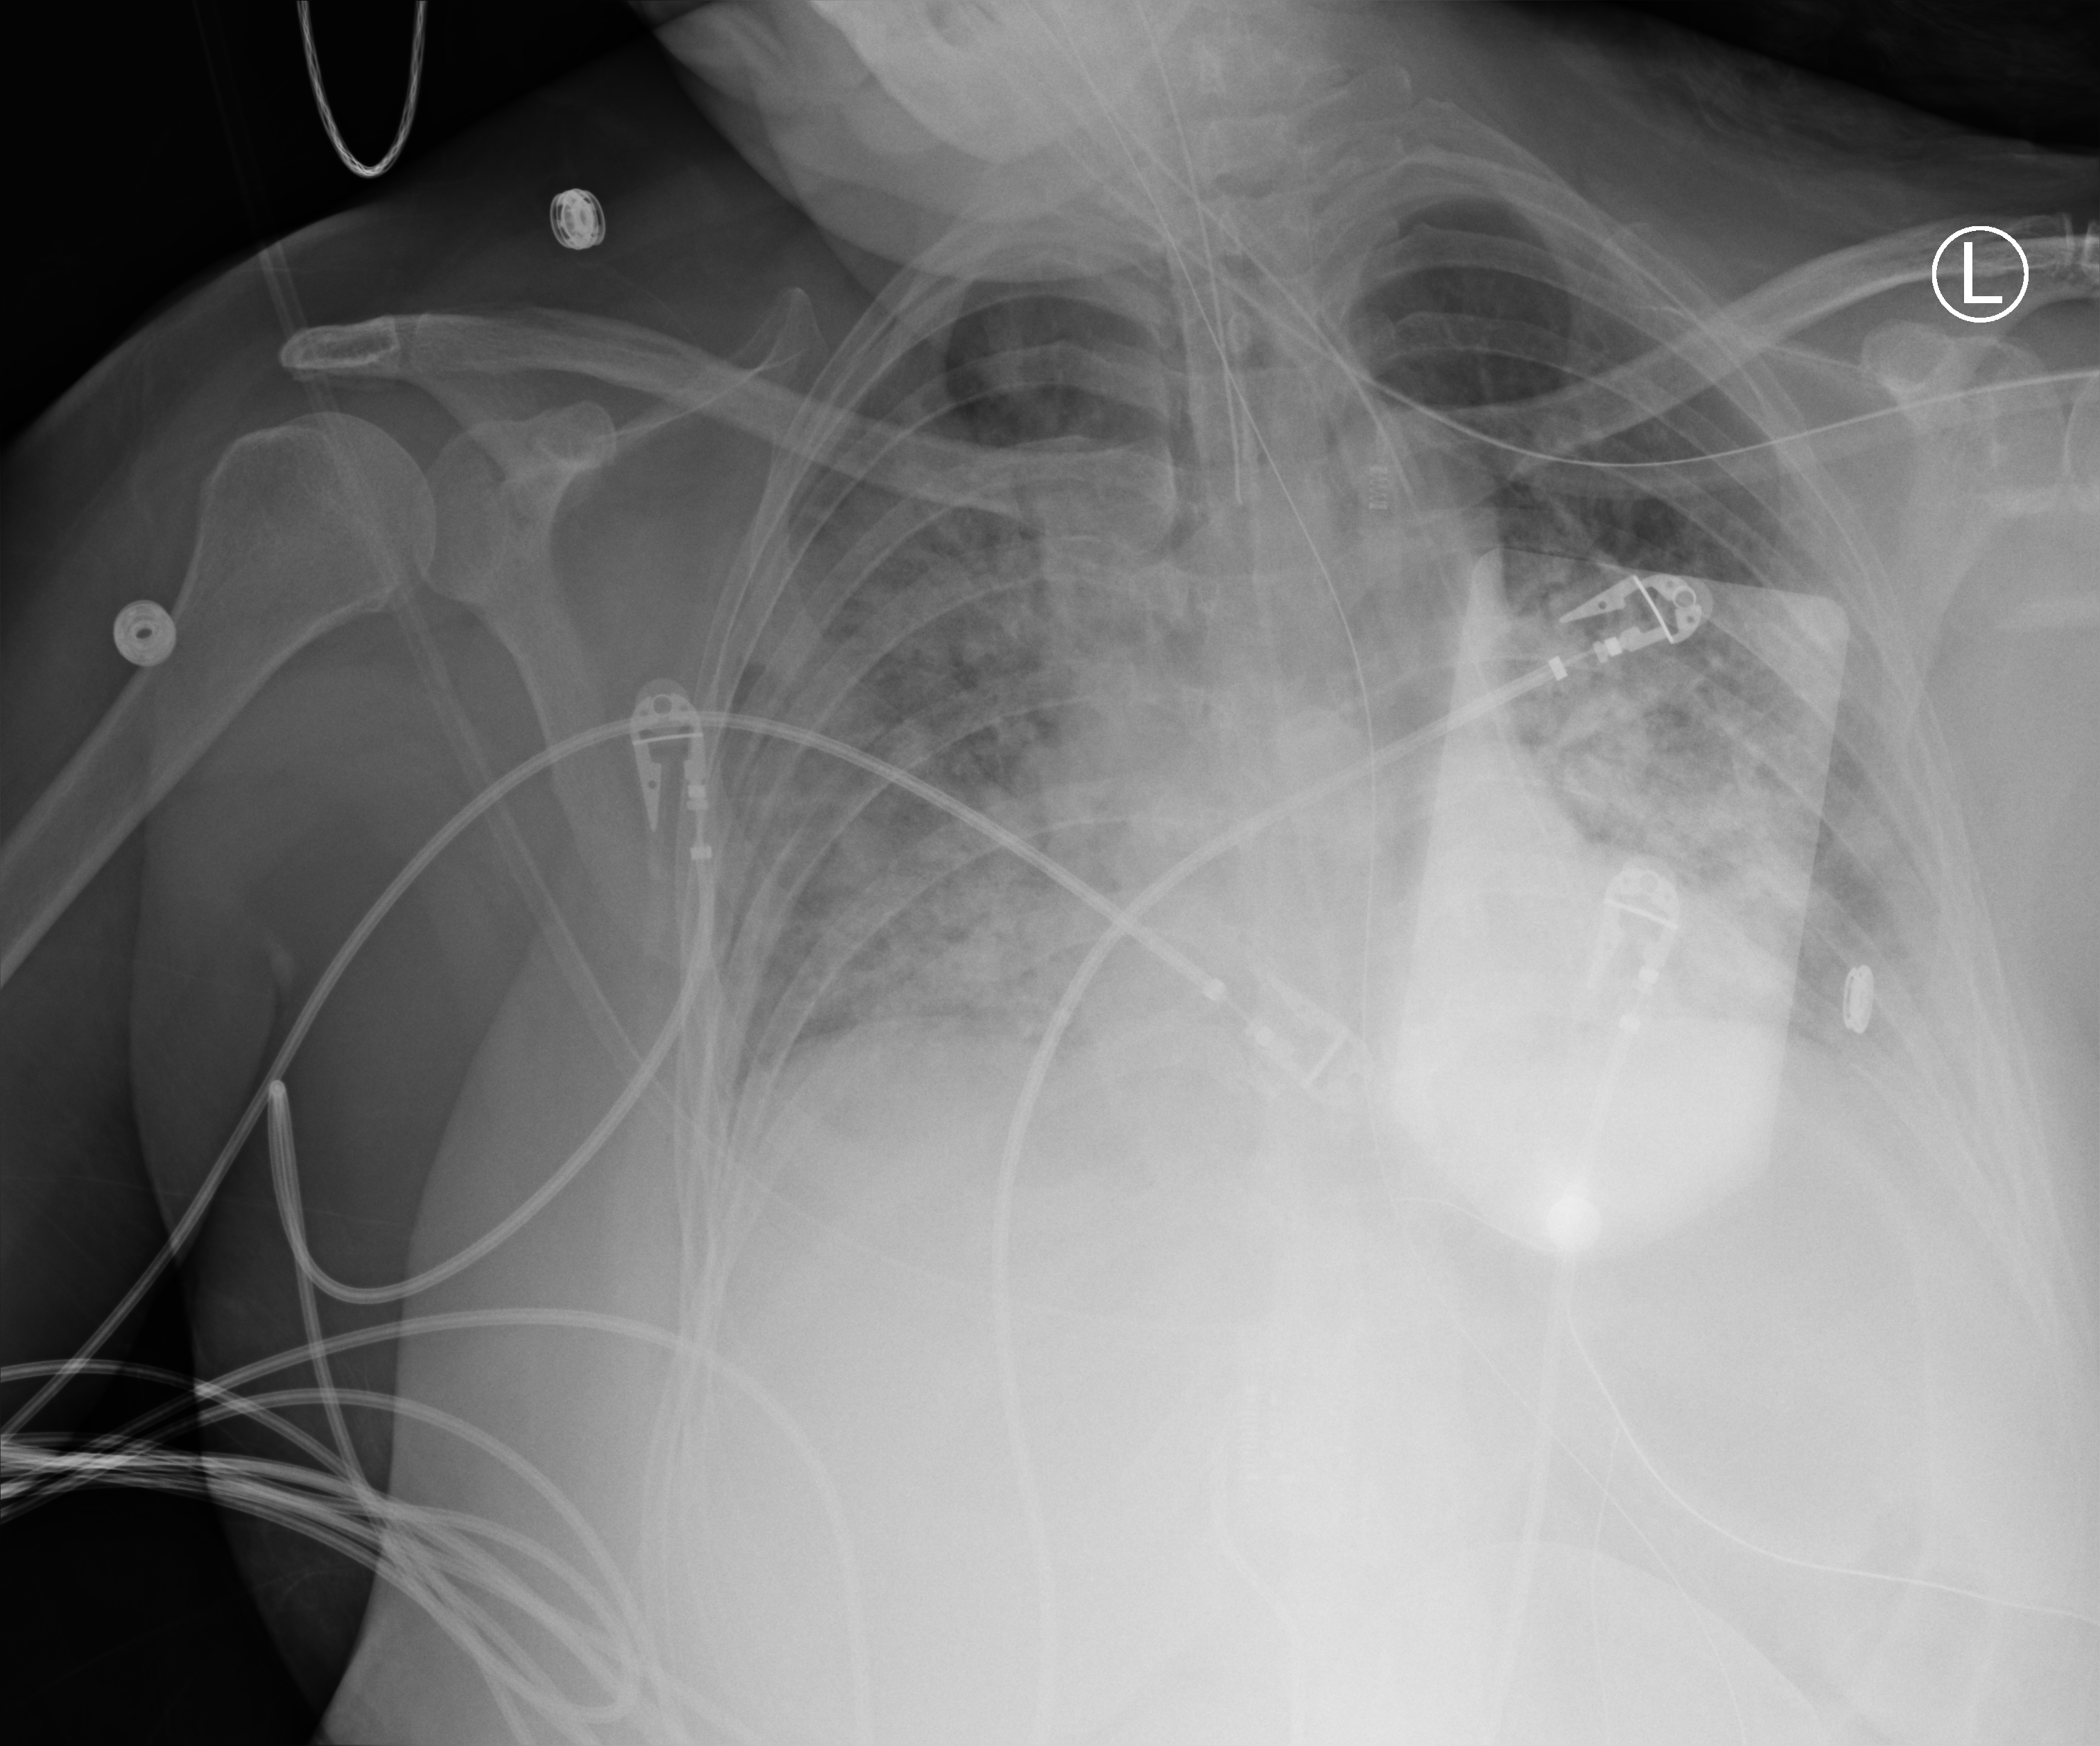
Portable chest radiograph, anteroposterior (AP) projection. Female patient hospitalised with COVID-19, age 18–59 years.
Admission-level facts for this patient (not findings on this image; timing relative to this image not recorded):
- mechanically ventilated during this hospital stay: yes
- admitted to intensive care during this hospital stay: yes
- other chronic lung disease (admission record): no